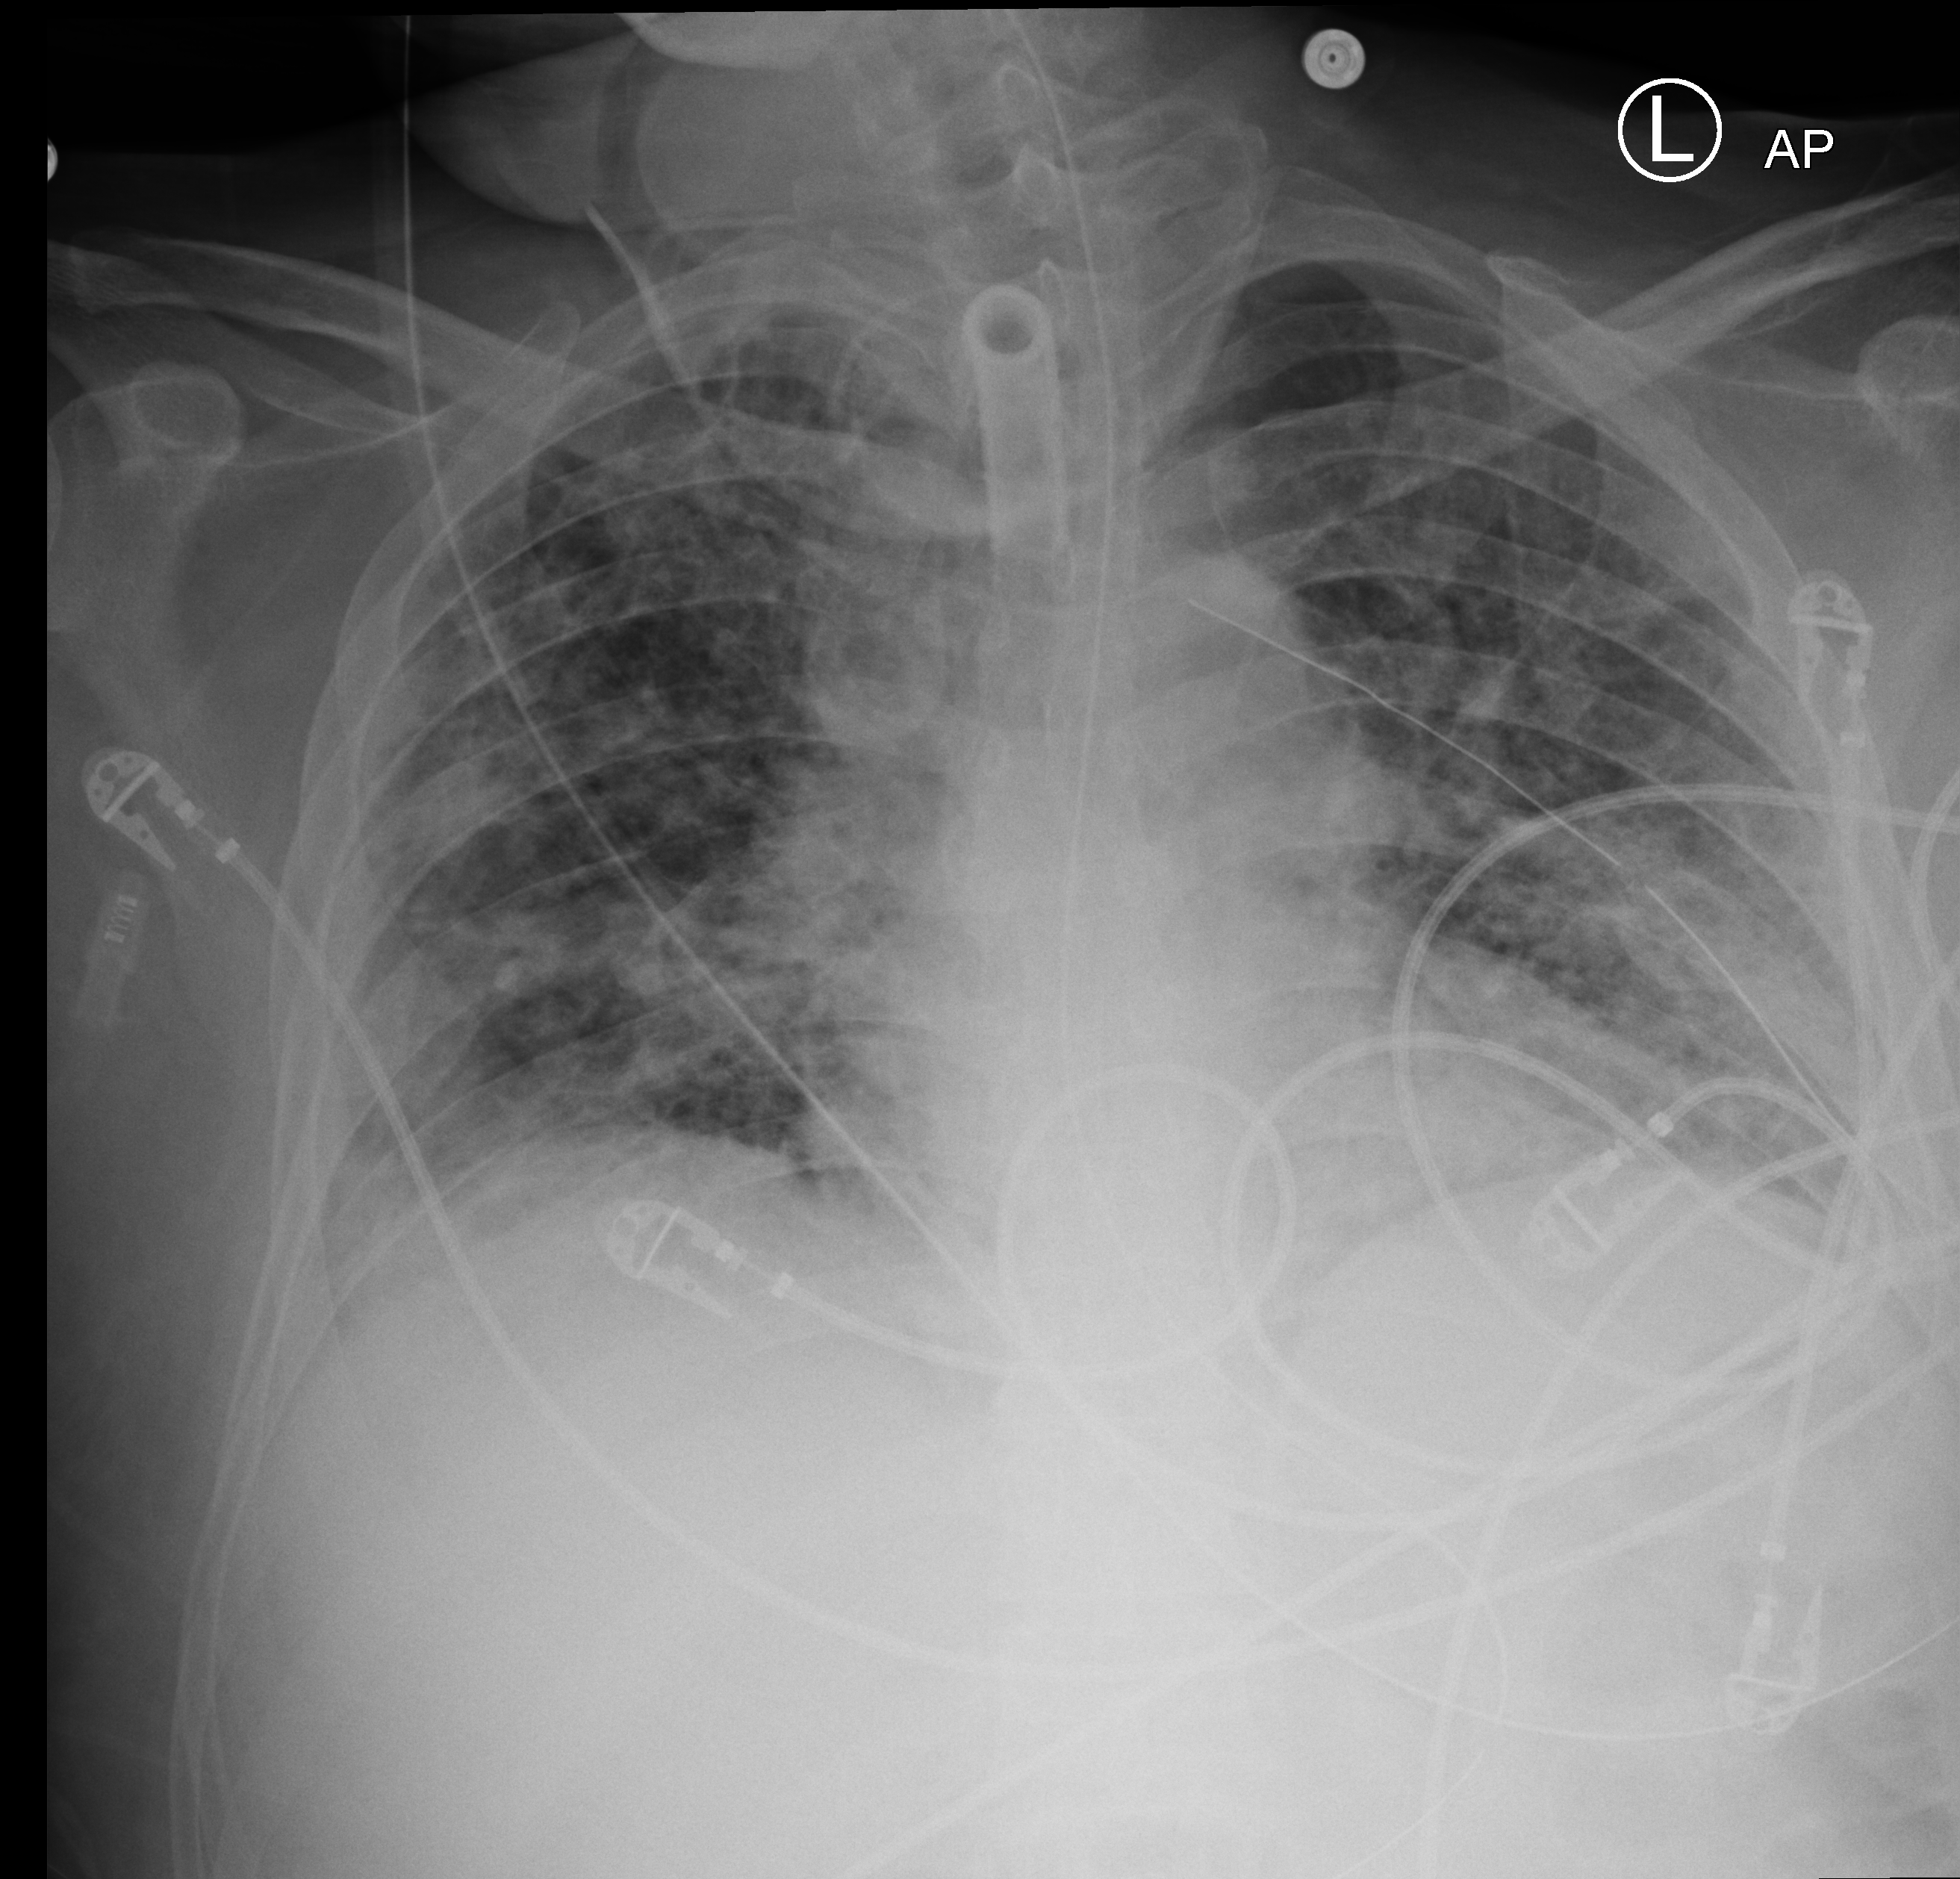
Bedside chest radiograph (computed radiography), anteroposterior (AP) projection. Male patient hospitalised with COVID-19, age 18–59 years.
Hospital-stay facts (about this admission, not read from this image; timing relative to this image not recorded): mechanically ventilated during this hospital stay: yes; chronic kidney disease (admission record): no; other chronic lung disease (admission record): no.